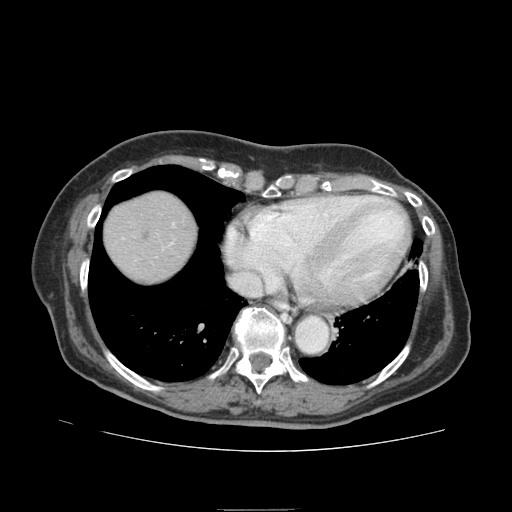
Contrast-enhanced abdominal CT (liver protocol), one axial slice. Slice 77 of 95 in the series (ordered by position). 140 kVp. Soft-tissue window (W 400 / L 40 HU). 2.5 mm slice thickness. 512 × 512 image matrix. Case-level facts recorded for this patient, not image findings: diagnosis: hepatocellular carcinoma (patient treated with transarterial chemoembolisation; whether this scan precedes or follows treatment is not stated here); TNM stage (as recorded): Stage-IVA; Child-Pugh class: B; tumour differentiation: moderately differentiated; tumour nodularity: uninodular.
Annotated regions visible in this slice (semi-automatically segmented with operator editing):
- abdominal aorta: bounding box <296,317,328,352> (left, top, right, bottom; pixels)
- liver parenchyma outside the tumour (the mass and vessels are separate outlines, so this box may not span the whole liver): <104,192,196,282>